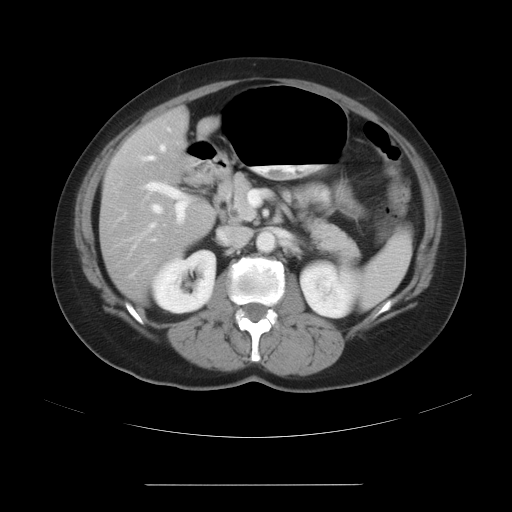
Contrast-enhanced abdominal CT, one axial slice; position 14 of 27 along the scan axis; reconstruction kernel STANDARD; 120 kVp; intravenous contrast given; soft-tissue window (W 400 / L 40 HU); 7.5 mm slice thickness; 512 × 512 image matrix, field of view 440 × 440 mm. Female patient, age 58 years. Case-level facts recorded for this patient, not image findings: diagnosis: colorectal cancer liver metastases, imaged before liver resection; multiple liver metastases: yes; largest metastasis: 1.9 cm; disease in both lobes: yes.
Outlined on this slice (outlined manually by an expert reader):
- hepatic veins: bounding box (x1, y1, x2, y2) in pixels: (125, 145, 165, 251)
- liver: (100, 111, 212, 296)
- planned liver remnant (the part of the liver to remain after resection): (106, 114, 210, 213)
- portal vein (with intrahepatic branches): (109, 126, 254, 278)